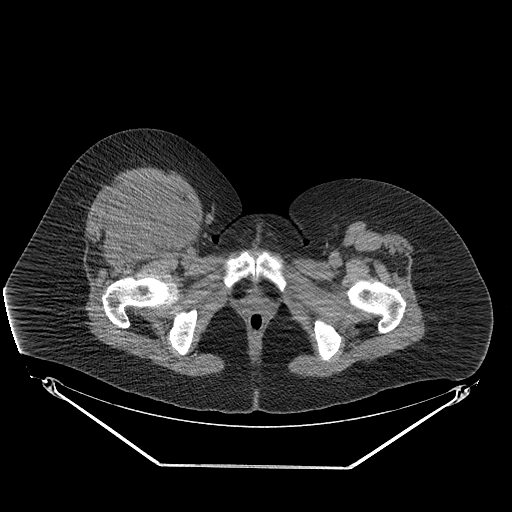
CT of an extremity soft-tissue mass (from a PET/CT study), one axial slice. Position 60 of 267 along the scan axis. Soft-tissue window (W 400 / L 40 HU). 3.75 mm slice thickness. 512 × 512 image matrix. Female patient. Case-level facts recorded for this patient, not image findings: histological type: malignant solitary fibrous tumor; grade: intermediate; site of the primary tumour: right thigh.
Annotated regions visible in this slice (expert contour drawn on MRI and transferred to this co-registered scan by the dataset authors):
- gross tumour volume including surrounding oedema: box from (x=98, y=178) to (x=179, y=243) px
- gross tumour volume (mass): (x=100, y=181)–(x=179, y=241)